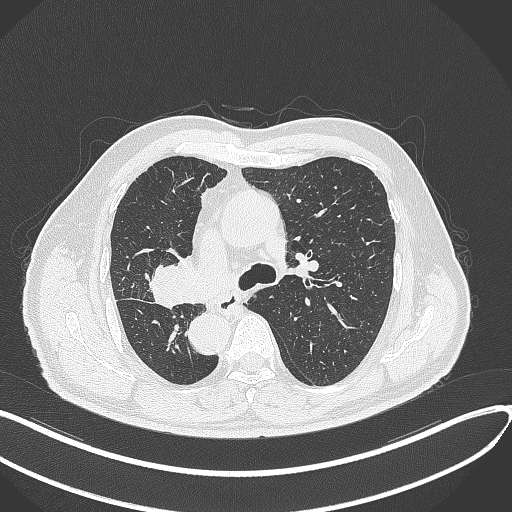
Chest CT, one axial slice; position 196 of 300 along the scan axis; reconstruction kernel B70f; 120 kVp; lung window (W 1500 / L -600 HU); 1 mm slice thickness; 512 × 512 image matrix, field of view 400 × 400 mm. Male patient, age 67 years. From the clinical record (not read from this slice): clinical TNM (as recorded): T2a N0 M0.
Outlined on this slice (rectangle marked by the reading radiologist):
- lung tumour (recorded histology: squamous cell carcinoma): bounding box (x1, y1, x2, y2) in pixels: (142, 253, 198, 309)